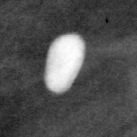
Region of interest cut from a scanned film mammogram (one marked finding); right breast; MLO view.
- Marked abnormality: calcifications, morphology coarse; BI-RADS assessment category 2; benign without callback (not worked up further).